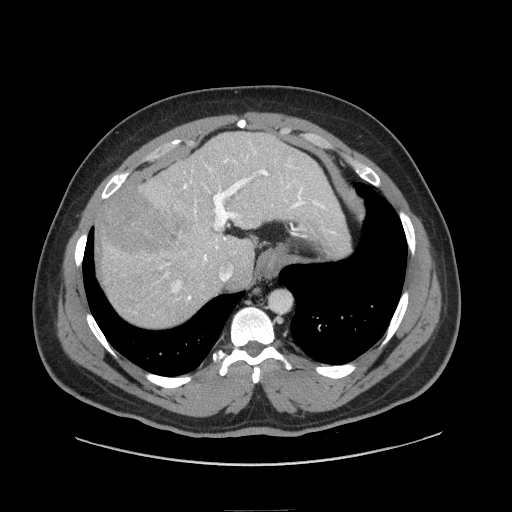
Contrast-enhanced abdominal CT (liver protocol), one axial slice; position 61 of 87 along the scan axis; 140 kVp; soft-tissue window (W 400 / L 40 HU); 512 × 512 image matrix. From the clinical record (not read from this slice): diagnosis: hepatocellular carcinoma (patient treated with transarterial chemoembolisation; whether this scan precedes or follows treatment is not stated here); TNM stage (as recorded): Stage-II; Child-Pugh class: A; tumour differentiation: moderately differentiated.
Structures marked on this image (semi-automatically segmented with operator editing):
- liver parenchyma outside the tumour (the mass and vessels are separate outlines, so this box may not span the whole liver): bounding box <98,132,338,326> (left, top, right, bottom; pixels)
- mass: <98,187,198,258>
- liver vessels: <160,151,326,300>